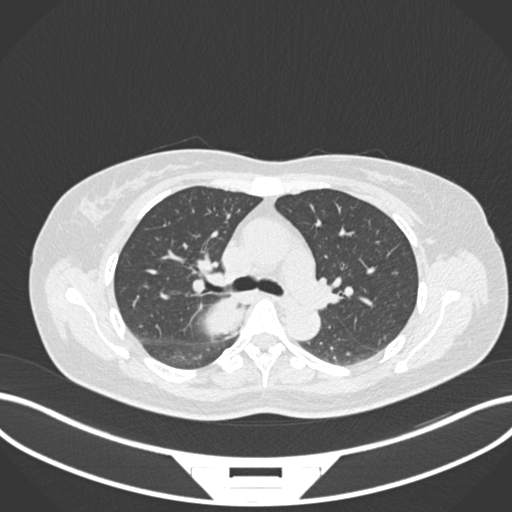
Chest CT, one axial slice. Slice 622 of 677 in the series (ordered by position). 120 kVp. Lung window (W 1500 / L -600 HU). 1 mm slice thickness. 512 × 512 image matrix, field of view 400 × 400 mm. Female patient, age 54 years. Case-level facts recorded for this patient, not image findings: clinical TNM (as recorded): T4 N0 M0.
Outlined on this slice (bounding box drawn by a radiologist):
- lung tumour (recorded histology: adenocarcinoma): box from (x=199, y=290) to (x=247, y=345) px